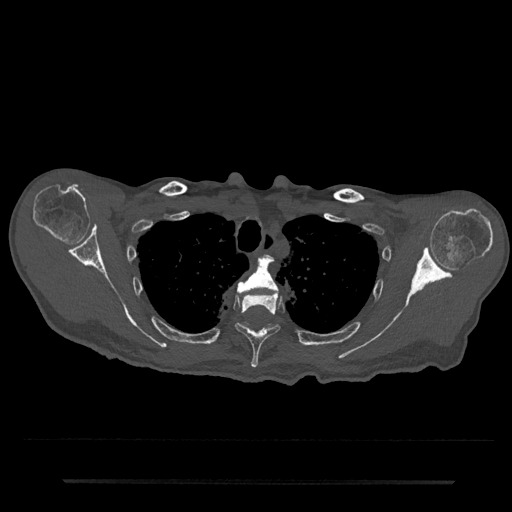
CT including the spine, one axial slice; slice 623 of 797 in the series (ordered by position); reconstruction kernel Br40s/3; bone window (W 1800 / L 400 HU); 0.5 mm slice thickness; 512 × 512 image matrix, field of view 427 × 427 mm. Male patient, age 74 years. Case-level facts recorded for this patient, not image findings: primary cancer: prostate.
Structures marked on this image (semi-automatically segmented with operator editing):
- T3 vertebra: bounding box (x1, y1, x2, y2) in pixels: (237, 256, 279, 294)
- T4 vertebra: (235, 293, 280, 368)
- T5 vertebra: (245, 322, 293, 341)